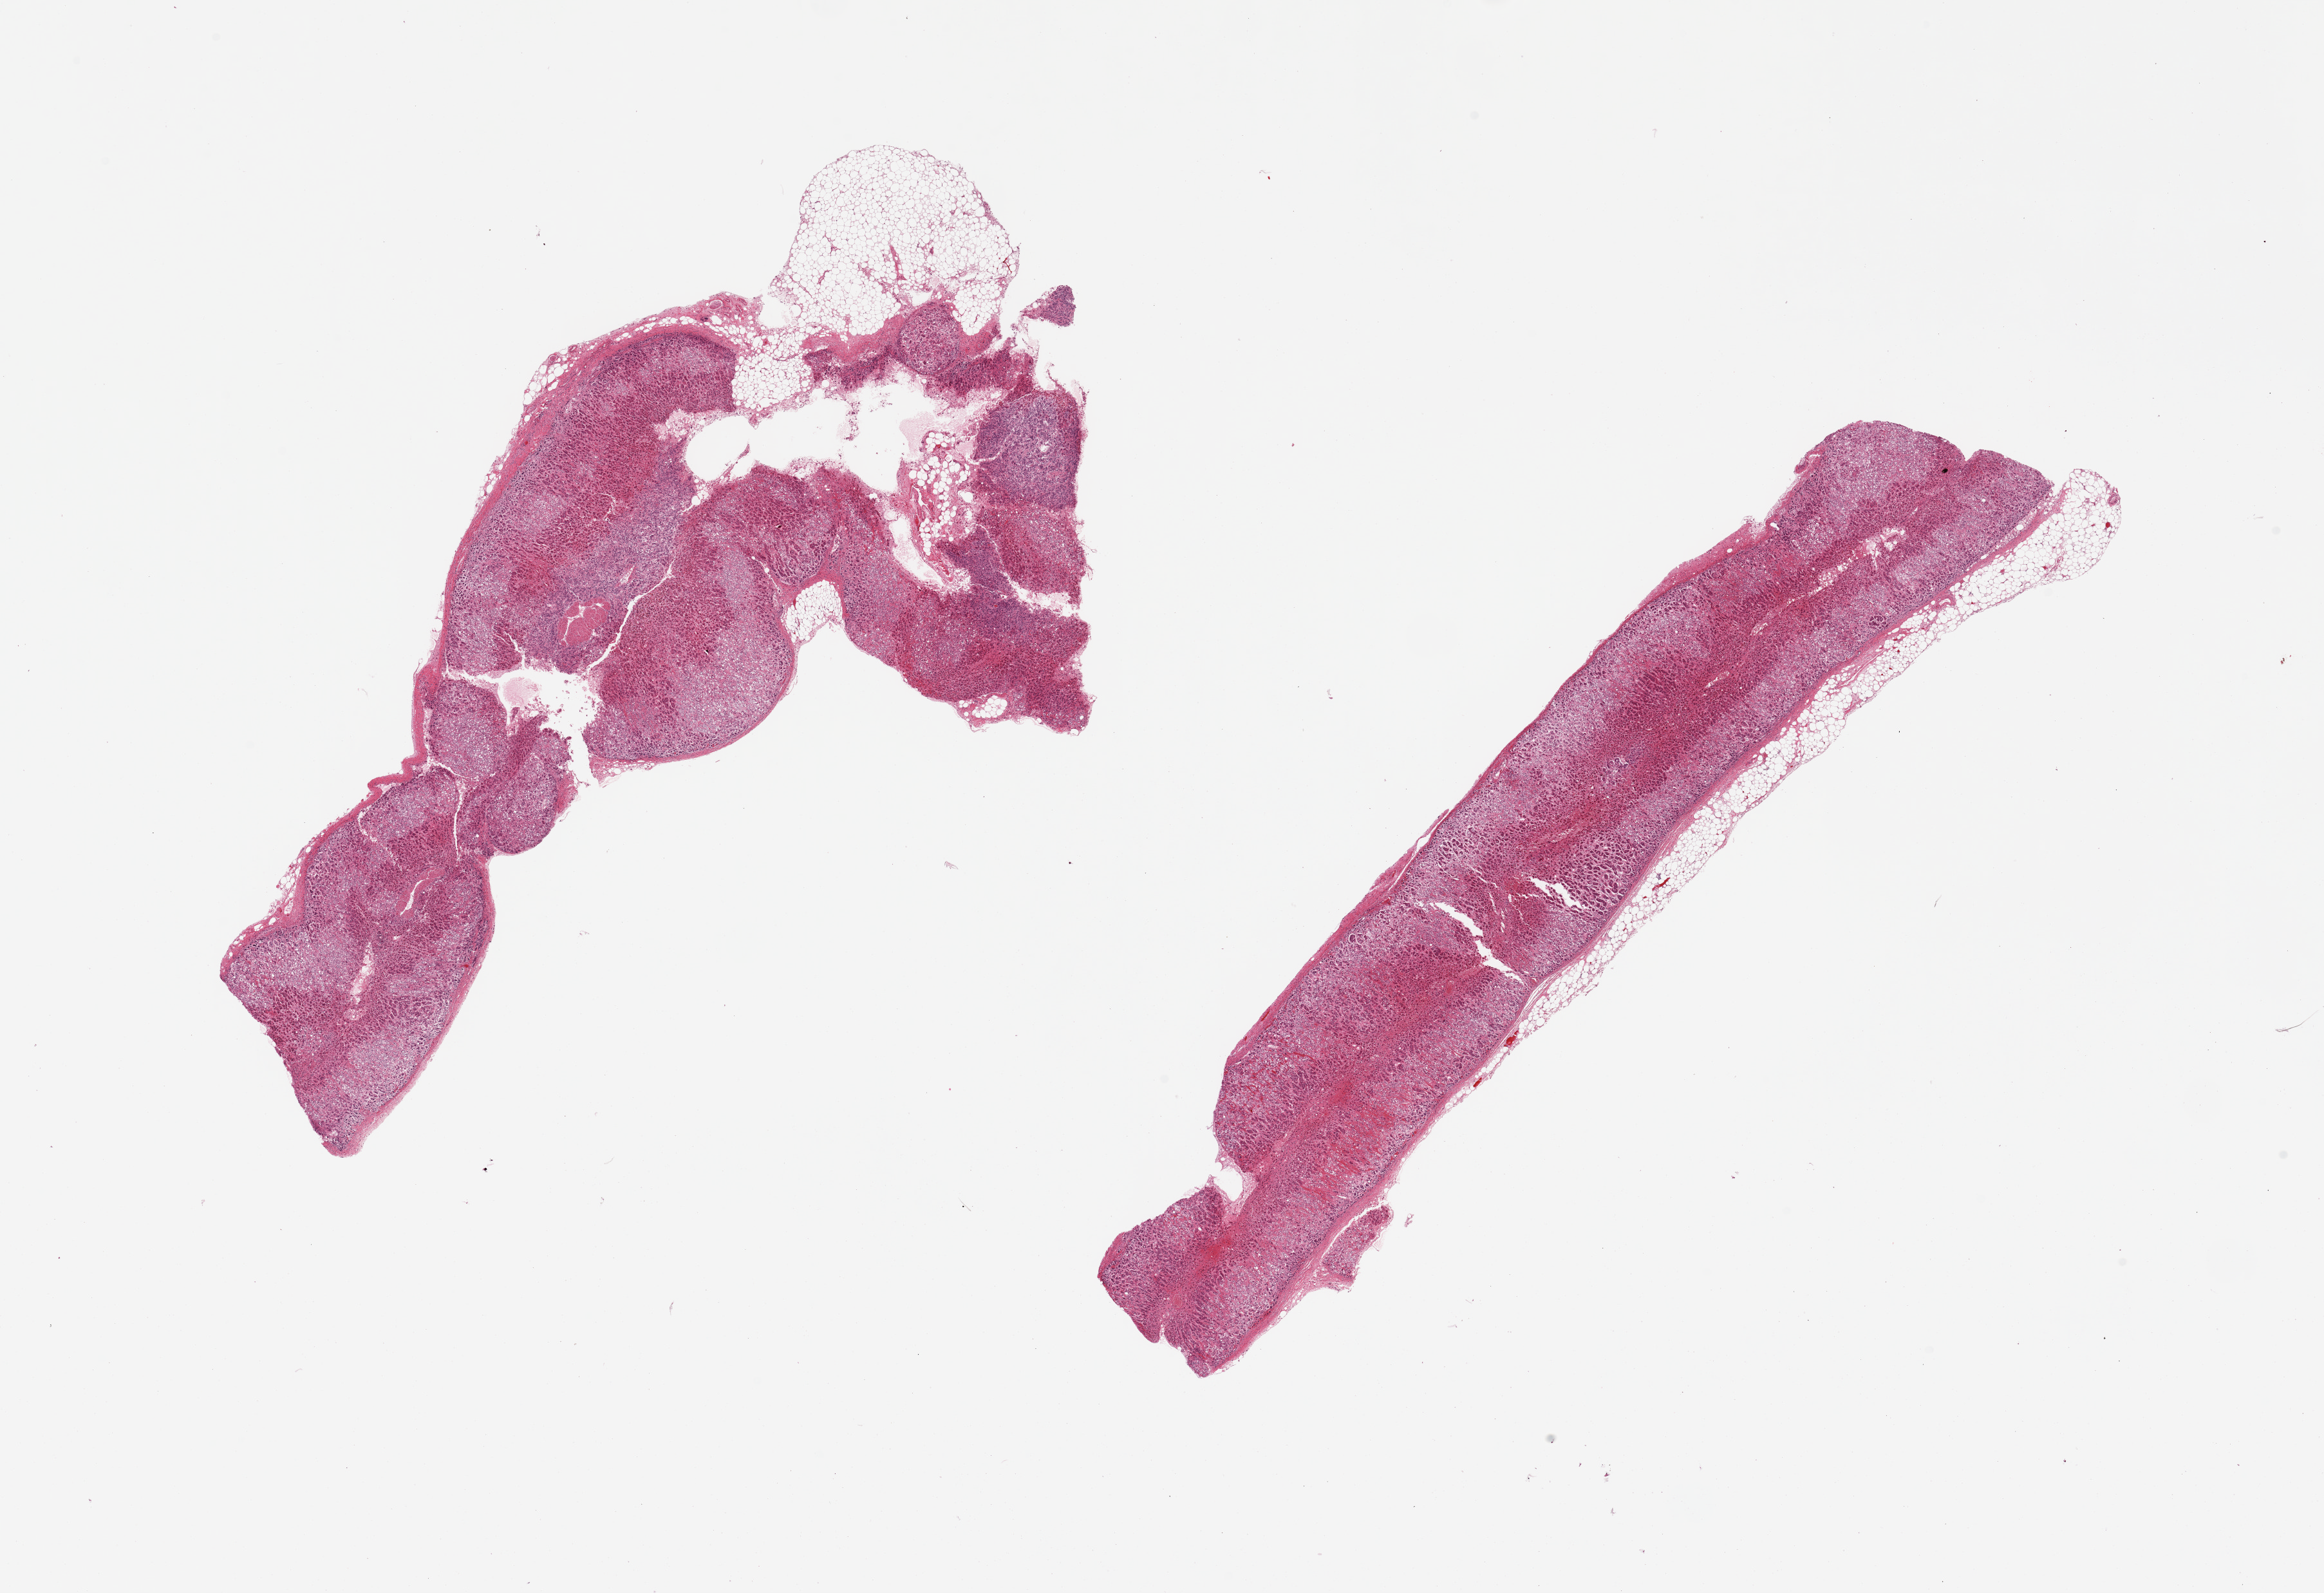
H&E whole-slide image — shown as a low-resolution overview of the whole scanned area (about 28.5 x 19.6 mm), PAXgene-fixed, paraffin-embedded tissue, target tissue: adrenal gland, donor tissue sample. Donor: female.
Reviewer comment on this tissue sample: 2 pieces, both with ~5-10% attached adipose tissue, hemorrhage.